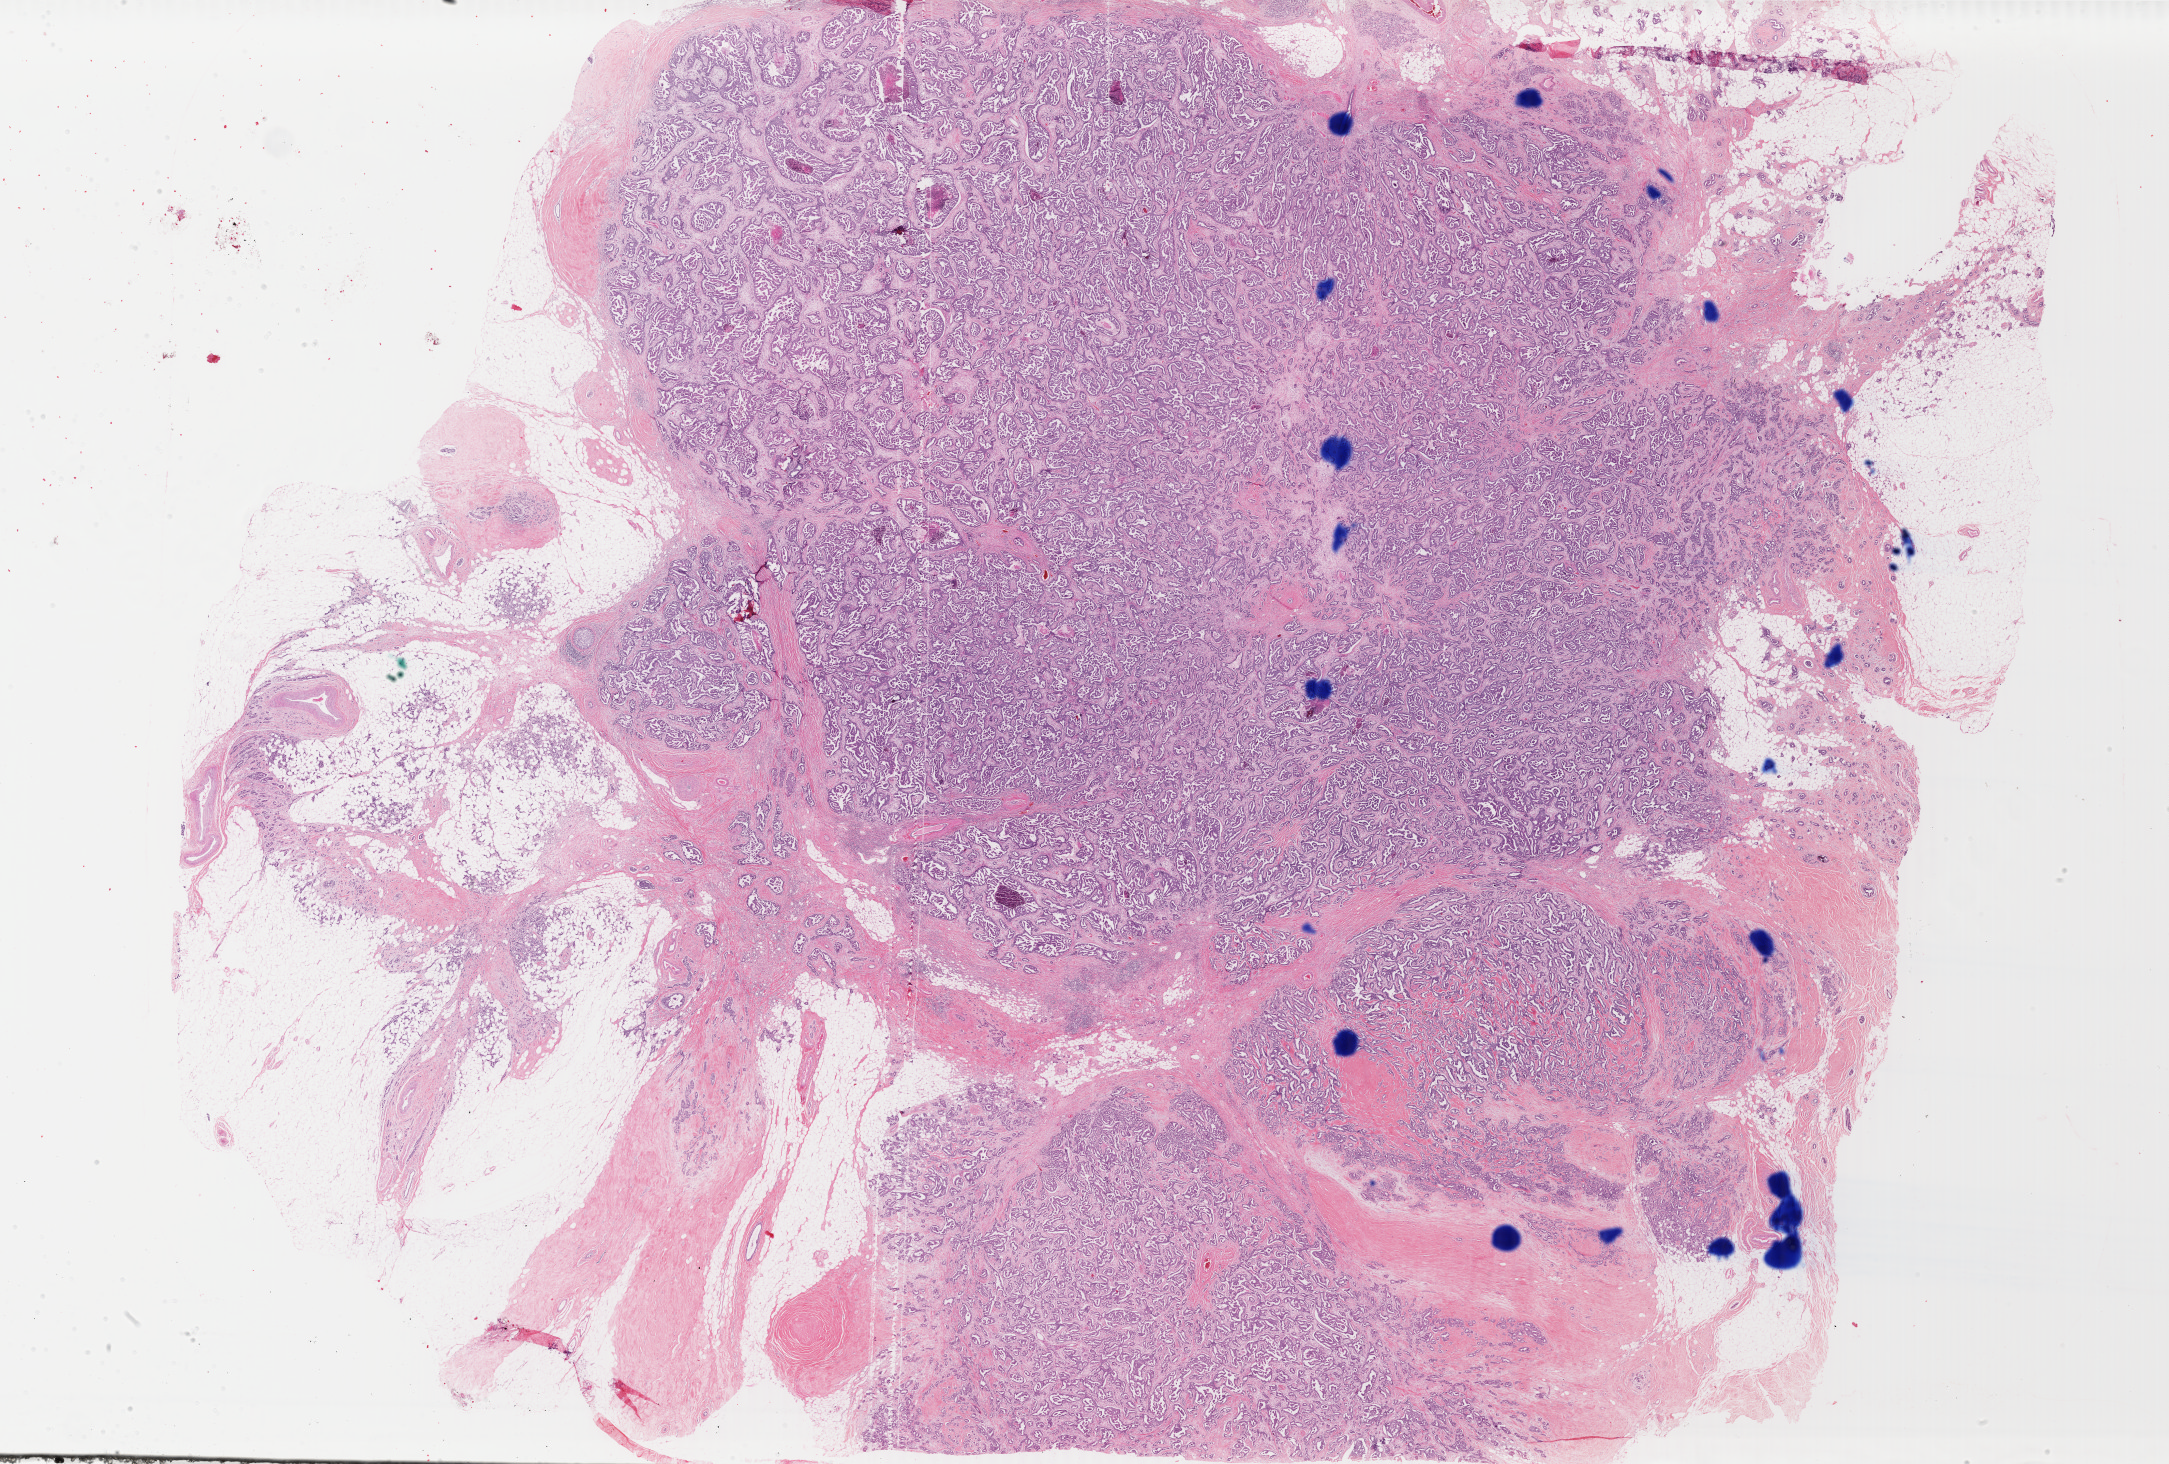
Digitized H&E tissue section (whole slide), a low-resolution overview of the entire scanned area, about 34.5 x 23.3 mm; formalin-fixed paraffin-embedded (FFPE) diagnostic section; breast, primary tumour sample. Female, age 75 years at initial diagnosis.
Pathologic diagnosis: Infiltrating duct mixed with other types of carcinoma. Lymph nodes positive (case pathology): 0 of 9 examined. Laterality: right. AJCC pathologic stage: IIB (4th edition).